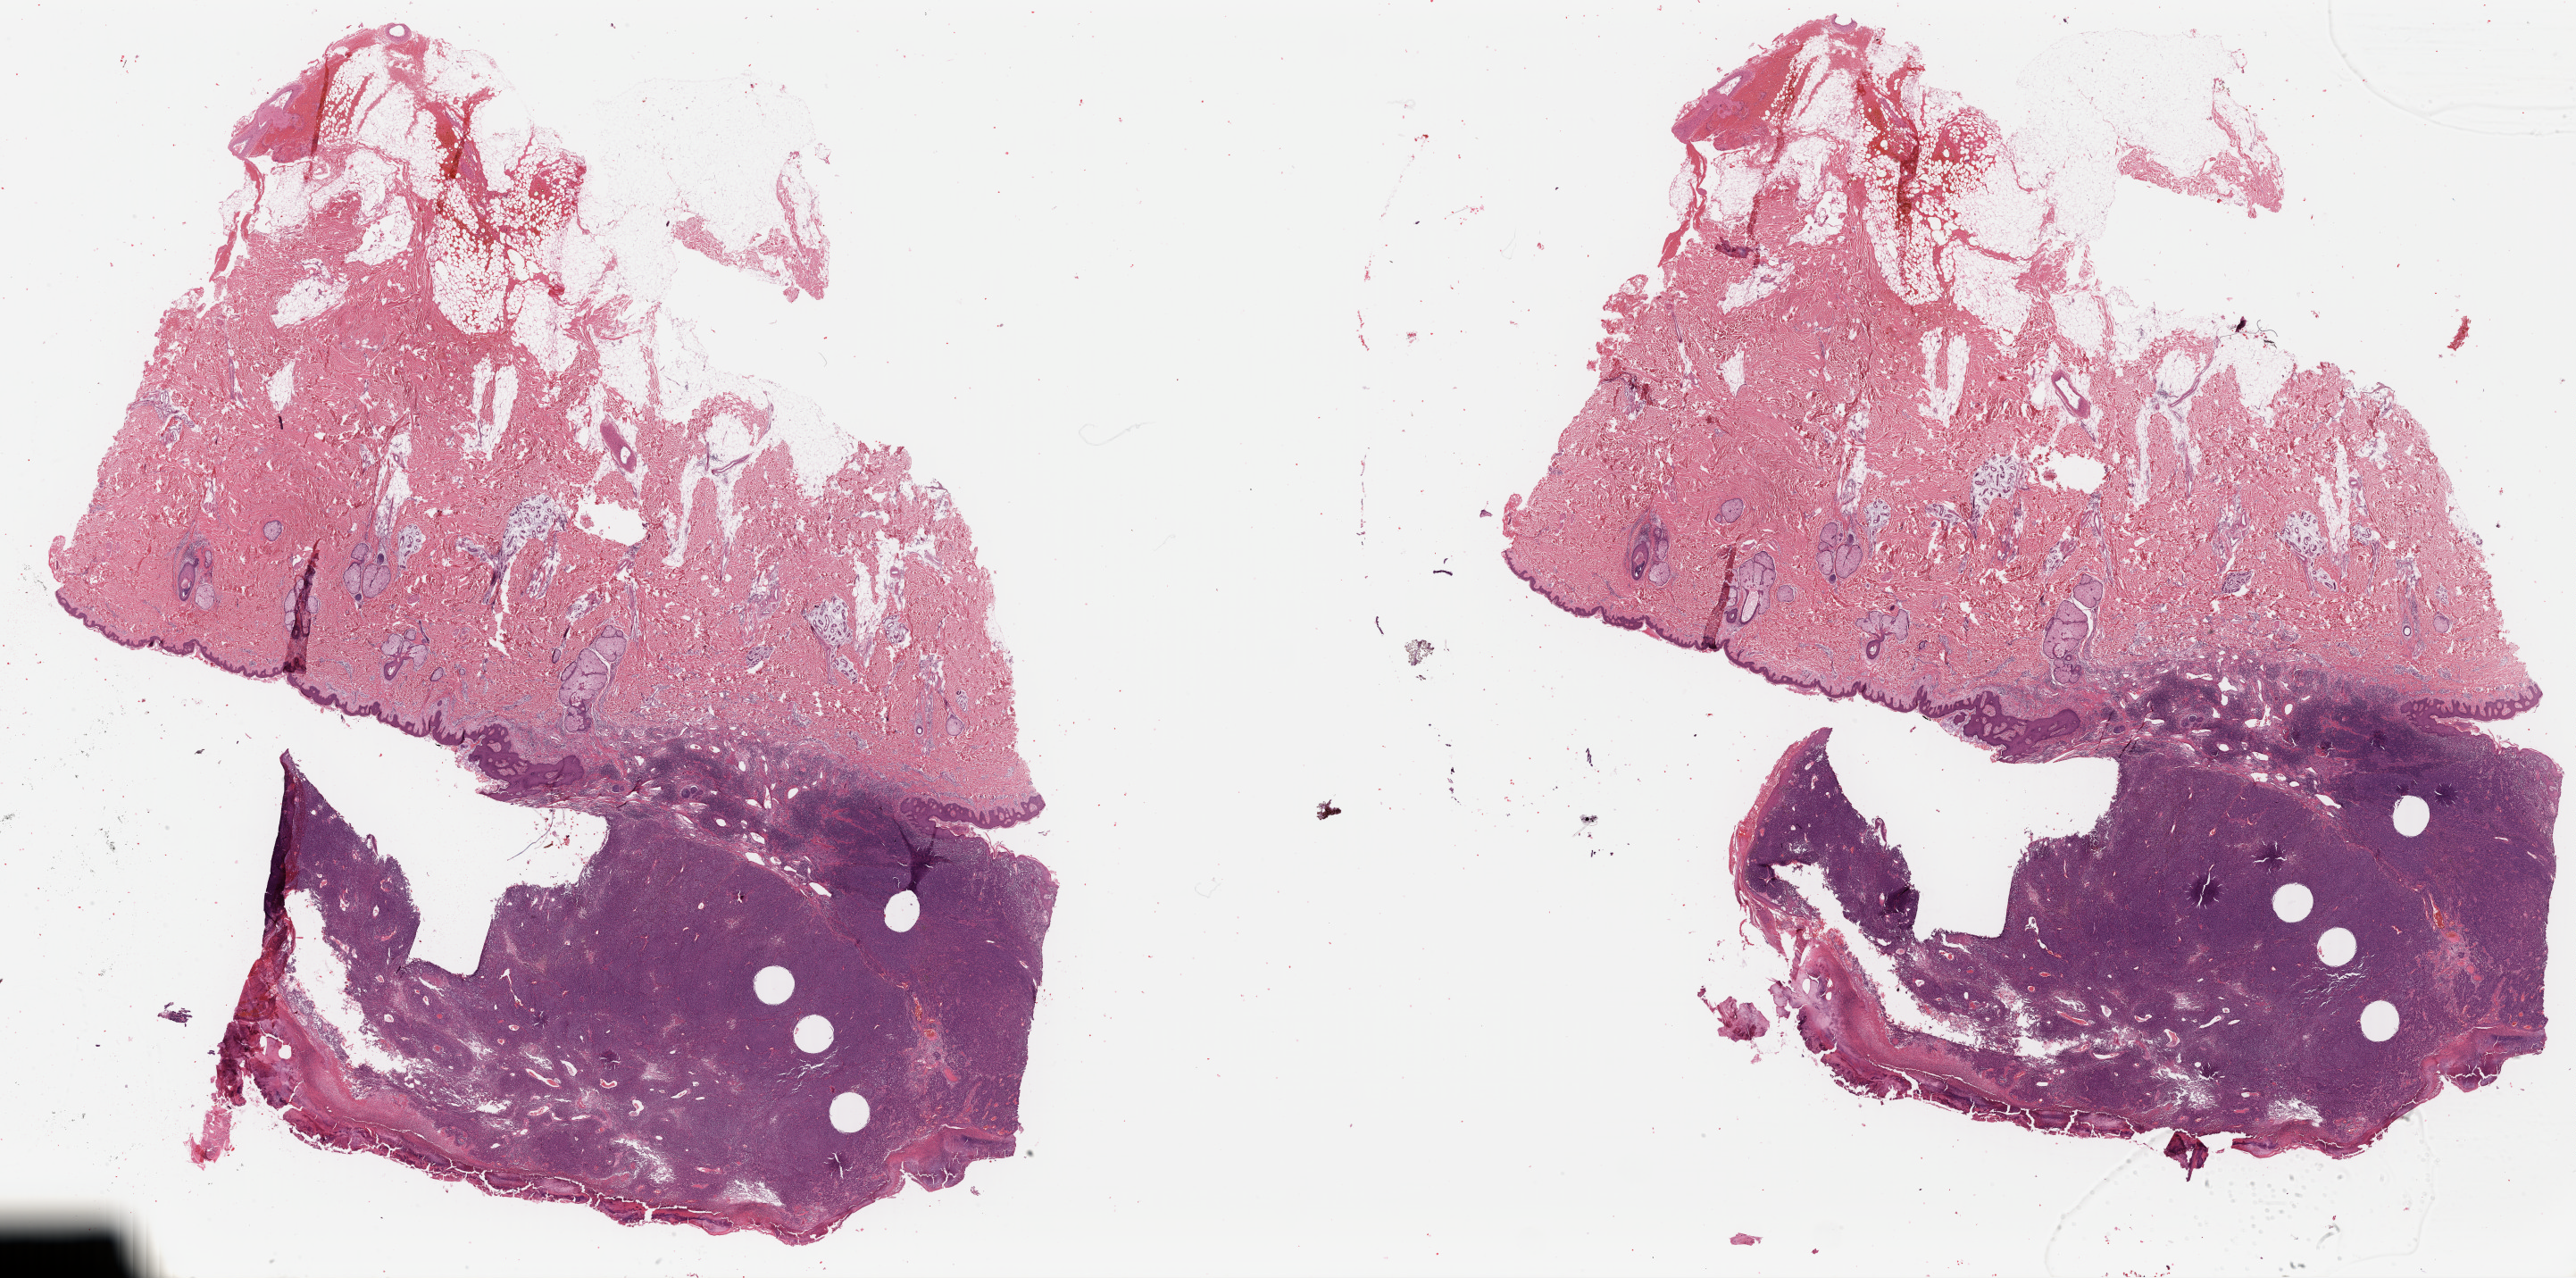
Hematoxylin and eosin (H&E) stained whole-slide image, shown as a low-resolution overview of the whole scanned area (about 45.4 x 22.5 mm, from a 40x scan), formalin-fixed paraffin-embedded (FFPE) diagnostic section, sample: primary tumour, skin. Male, age 43 years at initial diagnosis.
• diagnosis: Malignant melanoma, NOS
• AJCC pathologic stage: IIIA (5th edition)